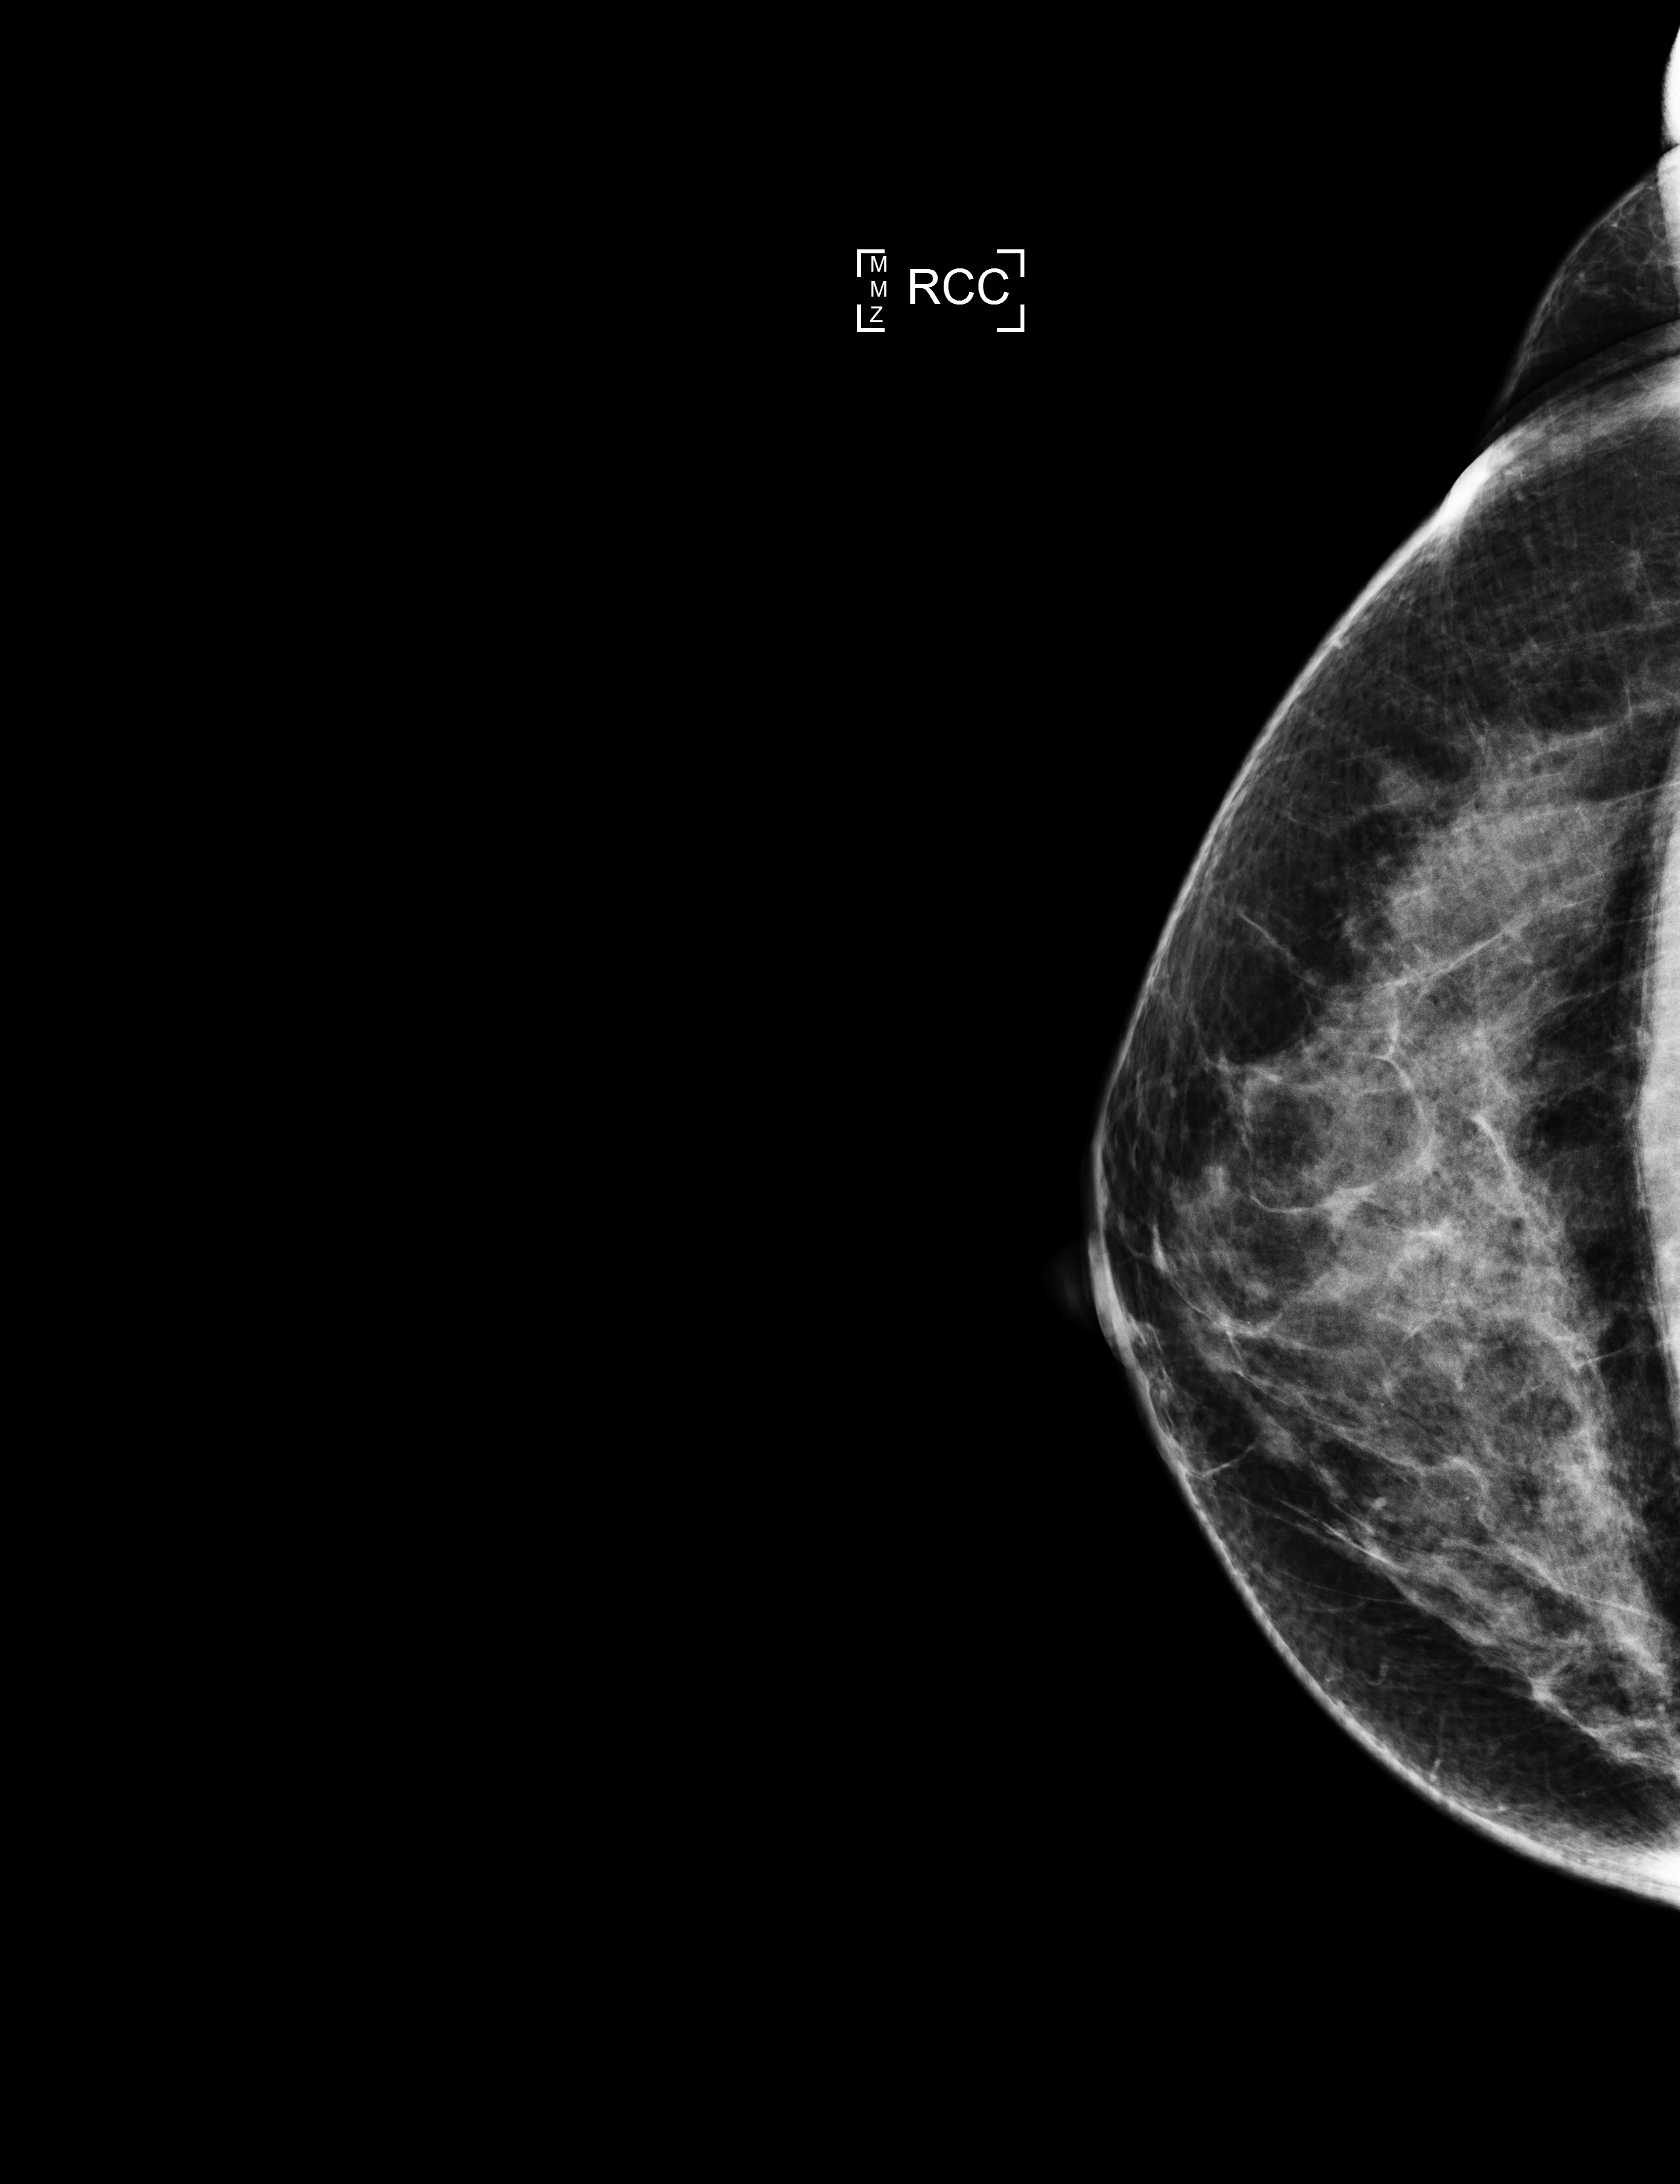
Full-field digital mammogram (FFDM), right breast, craniocaudal (CC) view, annual screening mammography examination, system: Selenia Dimensions. Patient: female, 47 years.
BI-RADS breast density category at the screening exam (both breasts, scale 1–4): 3. Final BI-RADS assessment for this screening round (tomosynthesis exam, both breasts): category 1. Recall: no recall after this screen.